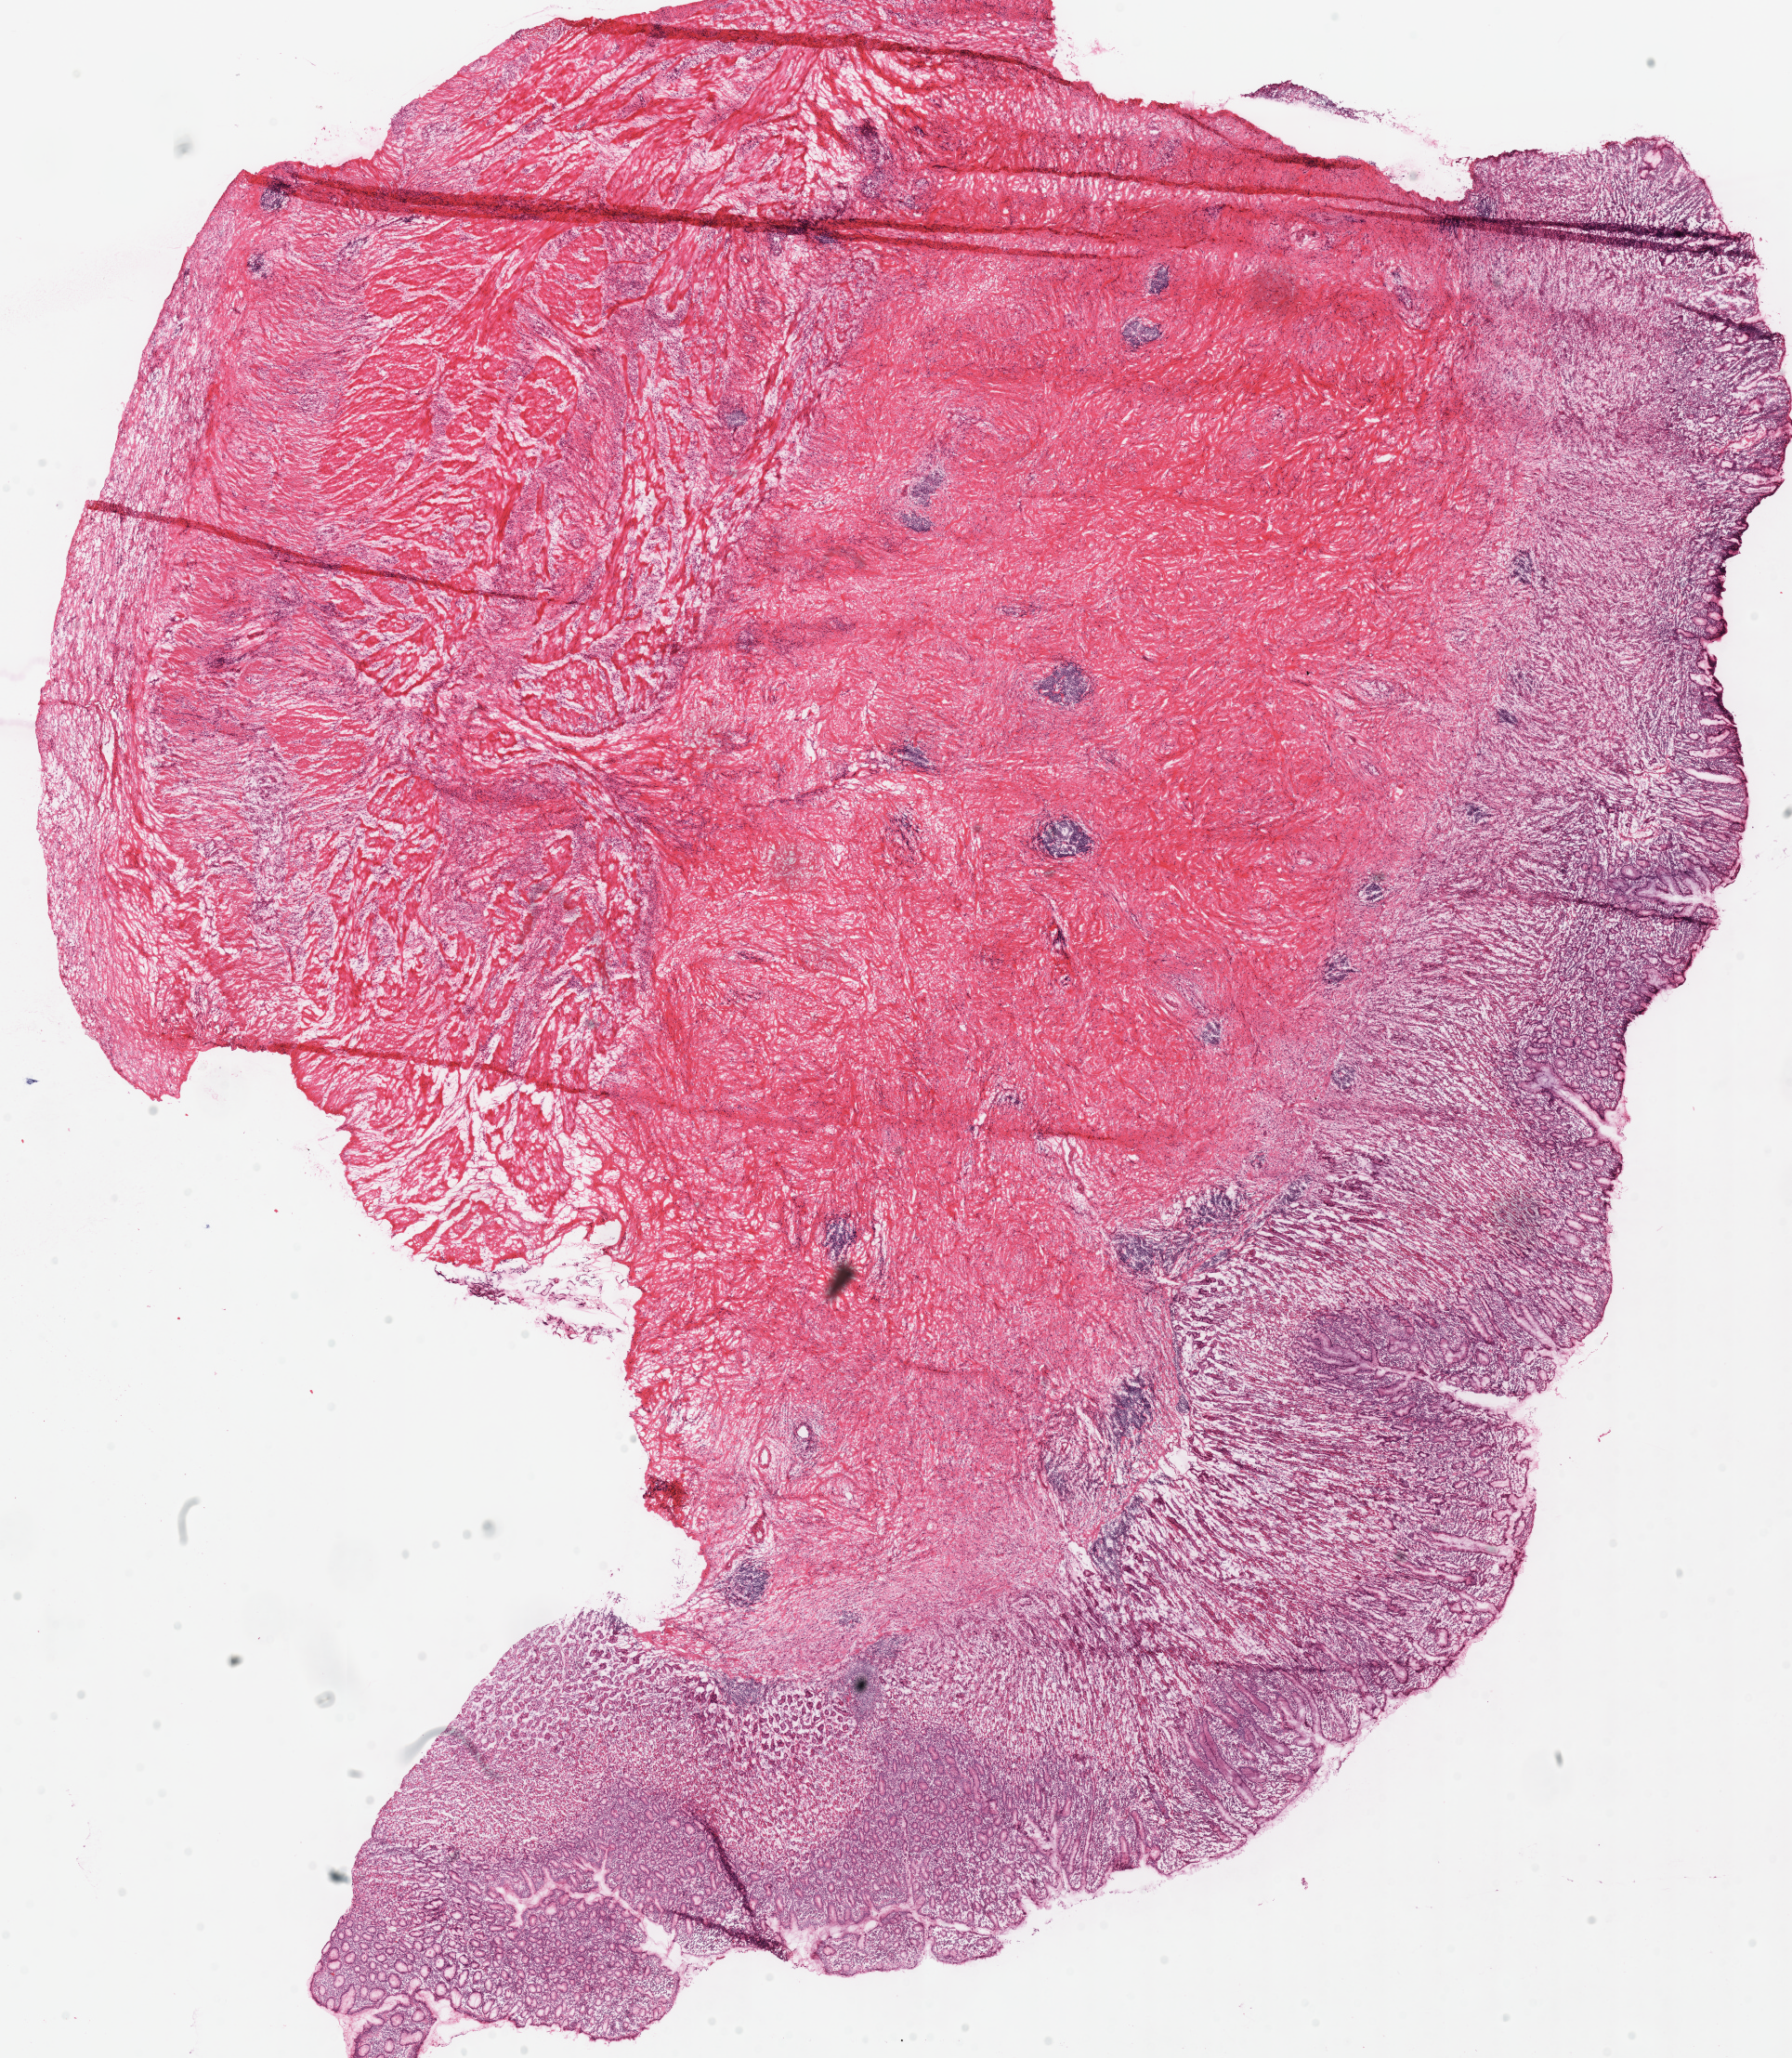
Whole-slide histology image, H&E, shown as a low-resolution overview of the whole scanned area (about 15.2 x 17.4 mm, acquisition: 40x scan), frozen section from the top of the tissue portion, stomach, primary tumour sample. Patient: female, age at initial diagnosis 42 years.
Histologic diagnosis: Carcinoma, diffuse type (fundus of stomach).